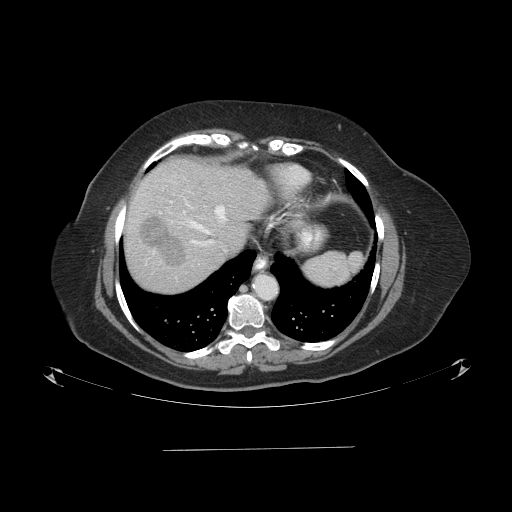
Contrast-enhanced abdominal CT (liver protocol), one axial slice; slice 76 of 103 in the series (ordered by position); reconstruction kernel STANDARD; one of 2 acquisitions stored at this slice position; soft-tissue window (W 400 / L 40 HU); 2.5 mm slice thickness; 512 × 512 image matrix, field of view 500 × 500 mm. Case-level facts recorded for this patient, not image findings: diagnosis: hepatocellular carcinoma (patient treated with transarterial chemoembolisation; whether this scan precedes or follows treatment is not stated here); TNM stage (as recorded): Stage-IIIA; Child-Pugh class: A; tumour differentiation: poorly differentiated; tumour nodularity: multinodular.
Outlined on this slice (semi-automatic segmentation, software-assisted and operator-edited):
- liver parenchyma outside the tumour (the mass and vessels are separate outlines, so this box may not span the whole liver): bounding box [x1, y1, x2, y2] px = [124, 158, 270, 292]
- mass: [140, 215, 187, 266]
- liver vessels: [153, 197, 227, 254]